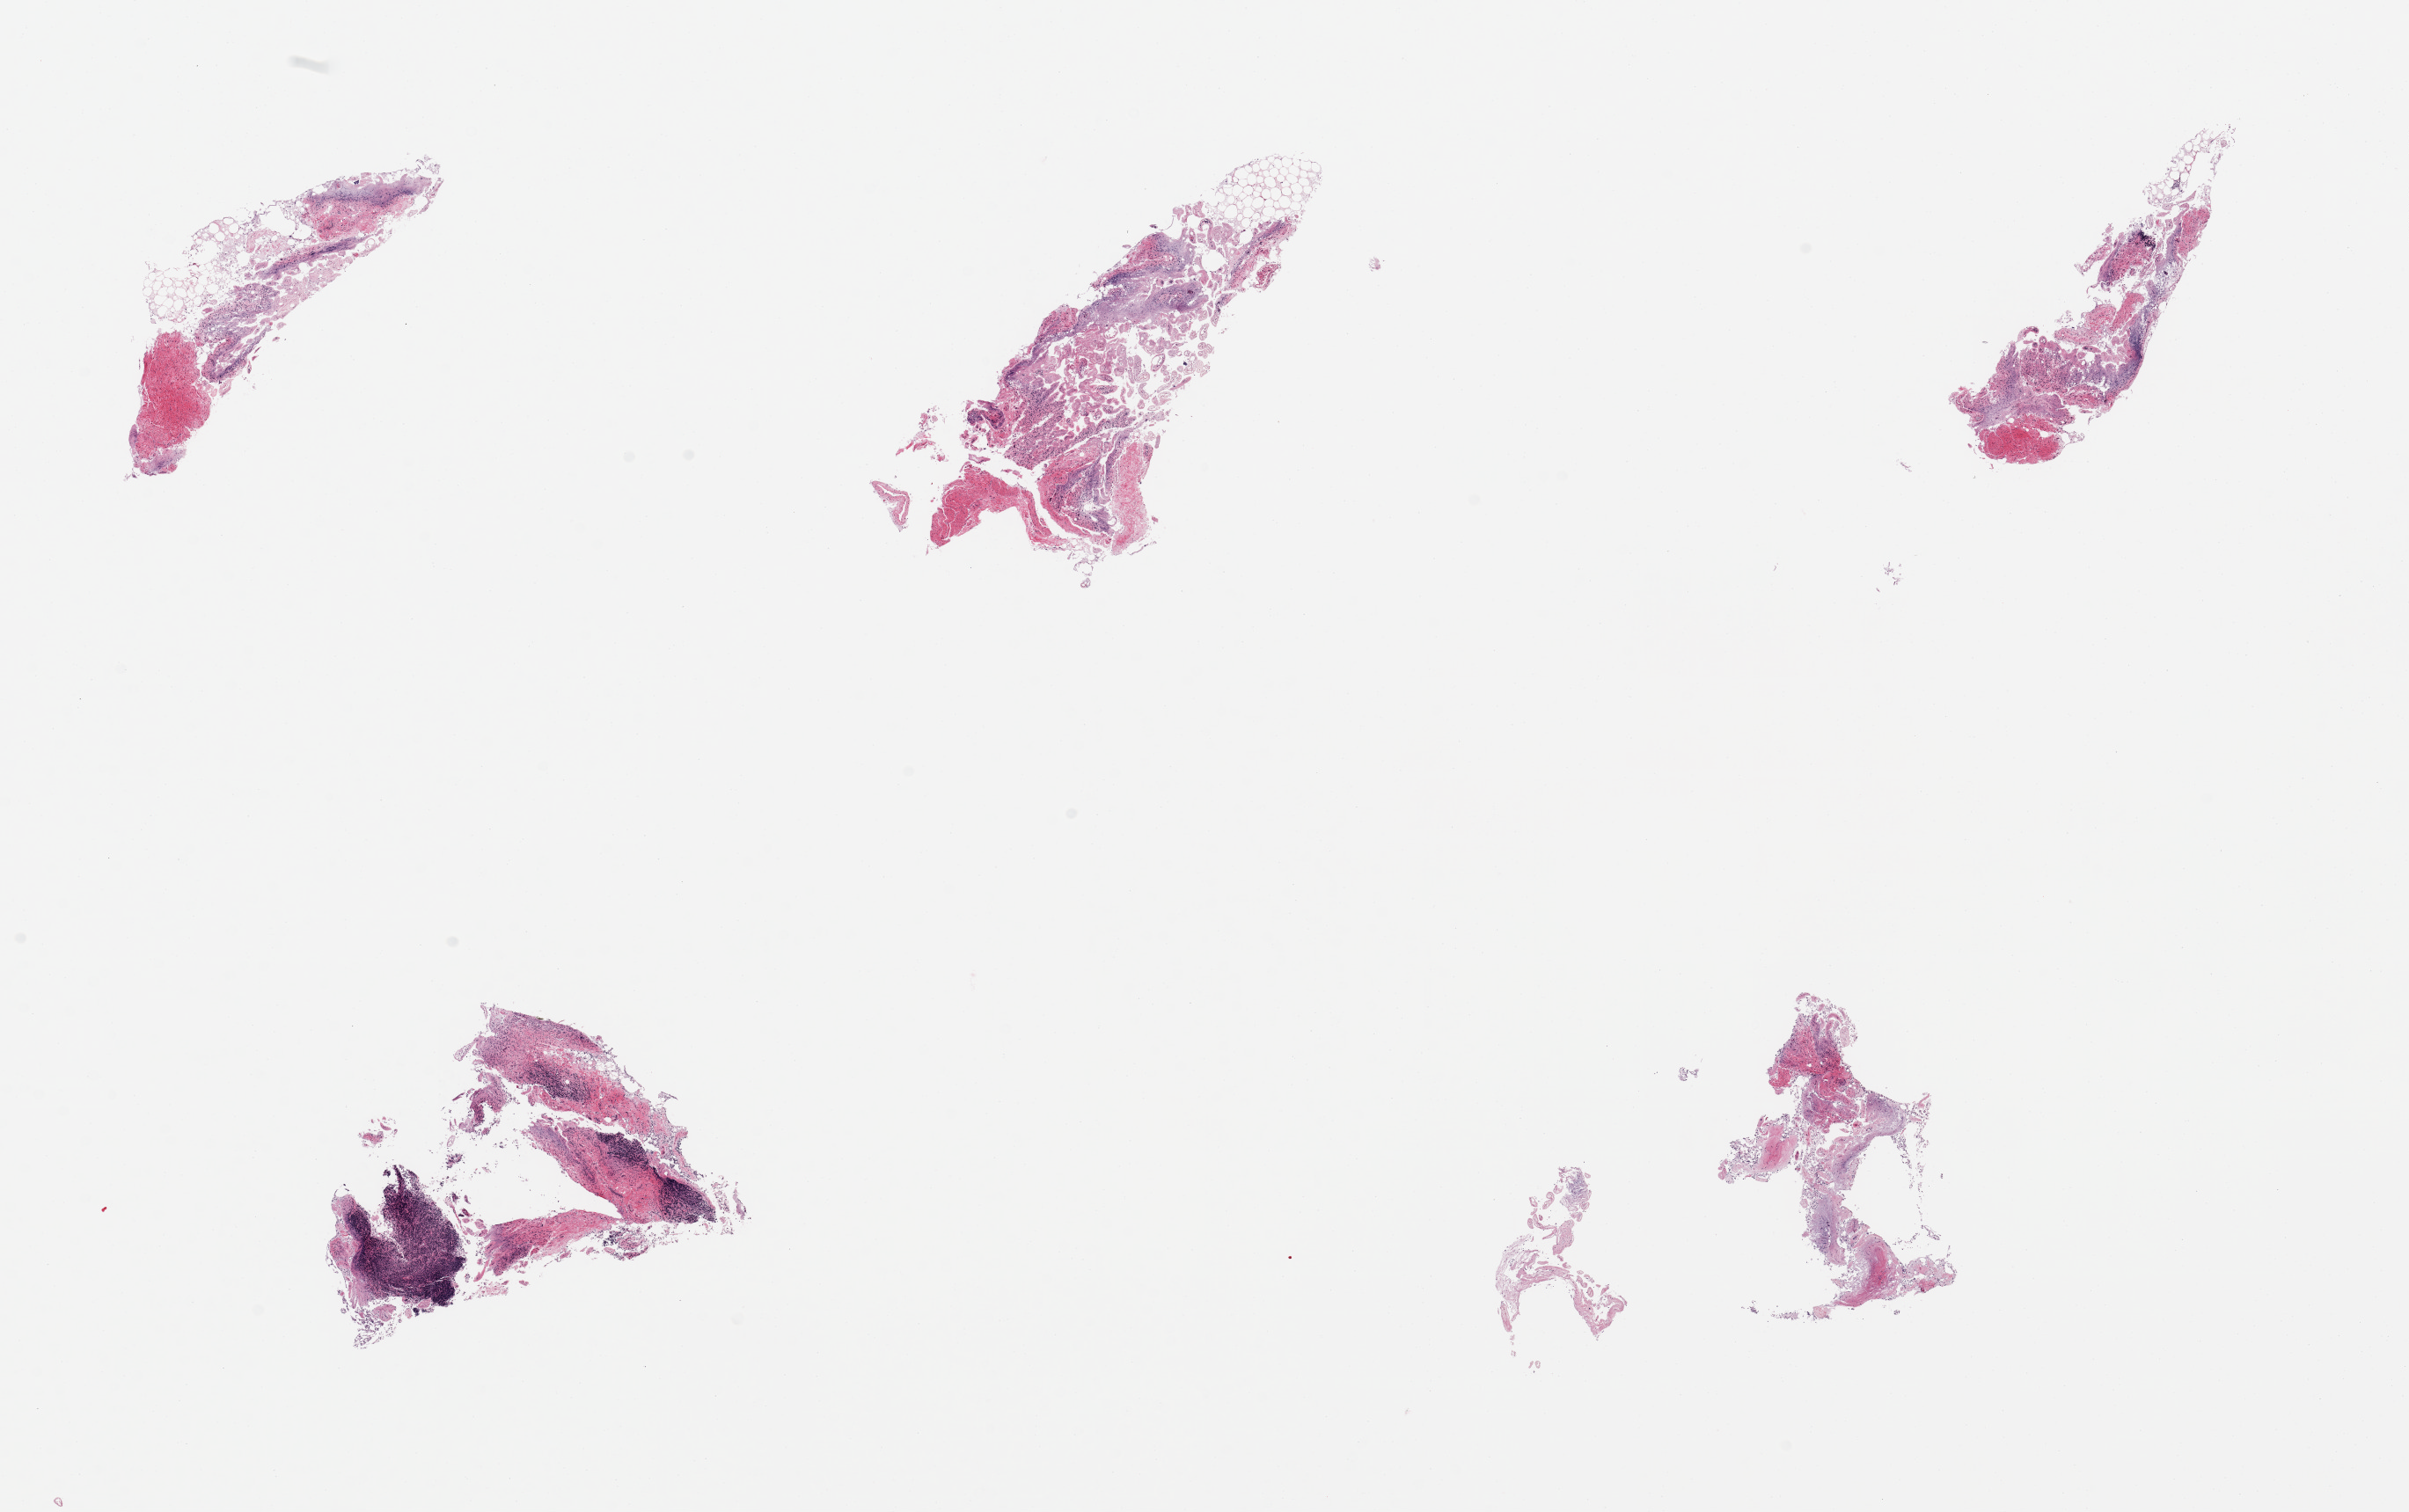
Digitized haematoxylin and eosin-stained section — a low-resolution overview of the entire scanned area, about 21.7 x 13.6 mm (slide scanned at 20x). PAXgene-fixed, paraffin-embedded tissue. Sampled site (target tissue): ileum. Donor tissue sample.
Pathologist's review note for this sample: 6 pieces, ~20% residual target lymphoid aggregates, glandular elements autolyszed/sloughed.